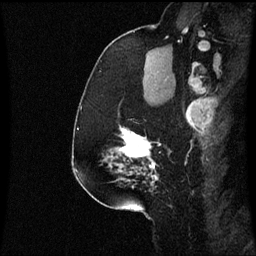
Breast MRI (dynamic contrast-enhanced), one sagittal slice; position 42 of 60 along the scan axis; dynamic contrast-enhanced series, image 2 of 3 at this slice position (ordered by acquisition); 1.5 T; TE 4.2 ms, TR 8.9 ms; 256 × 256 image matrix, field of view 200 × 200 mm. Patient: female, 58 years. From the clinical record (not read from this slice): setting: breast cancer imaged before/during neoadjuvant chemotherapy; receptor status: triple-negative.
Outlined on this slice (semi-automatically segmented with operator editing):
- analysis volume of interest (the breast-tissue region the enhancement analysis was run in; not a lesion): box from (x=104, y=128) to (x=171, y=179) px
- tumour enhancement mask (voxels above the 70 % enhancement threshold inside the analysis volume of interest): (x=120, y=128)–(x=159, y=179)